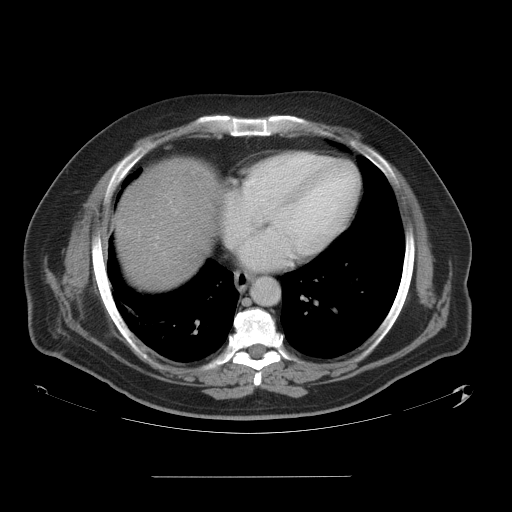
Contrast-enhanced abdominal CT, one axial slice. Slice 53 of 58 in the series (ordered by position). 120 kVp. Intravenous contrast given. Soft-tissue window (W 400 / L 40 HU). 5 mm slice thickness. 512 × 512 image matrix, field of view 480 × 480 mm. Male patient, age 63 years. Case-level facts recorded for this patient, not image findings: diagnosis: colorectal cancer liver metastases, imaged before liver resection; multiple liver metastases: no; largest metastasis: 4.2 cm.
Outlined on this slice (outlined manually by an expert reader):
- hepatic veins: box from (x=155, y=205) to (x=246, y=264) px
- liver: (x=115, y=158)–(x=217, y=291)
- planned liver remnant (the part of the liver to remain after resection): (x=115, y=217)–(x=207, y=291)